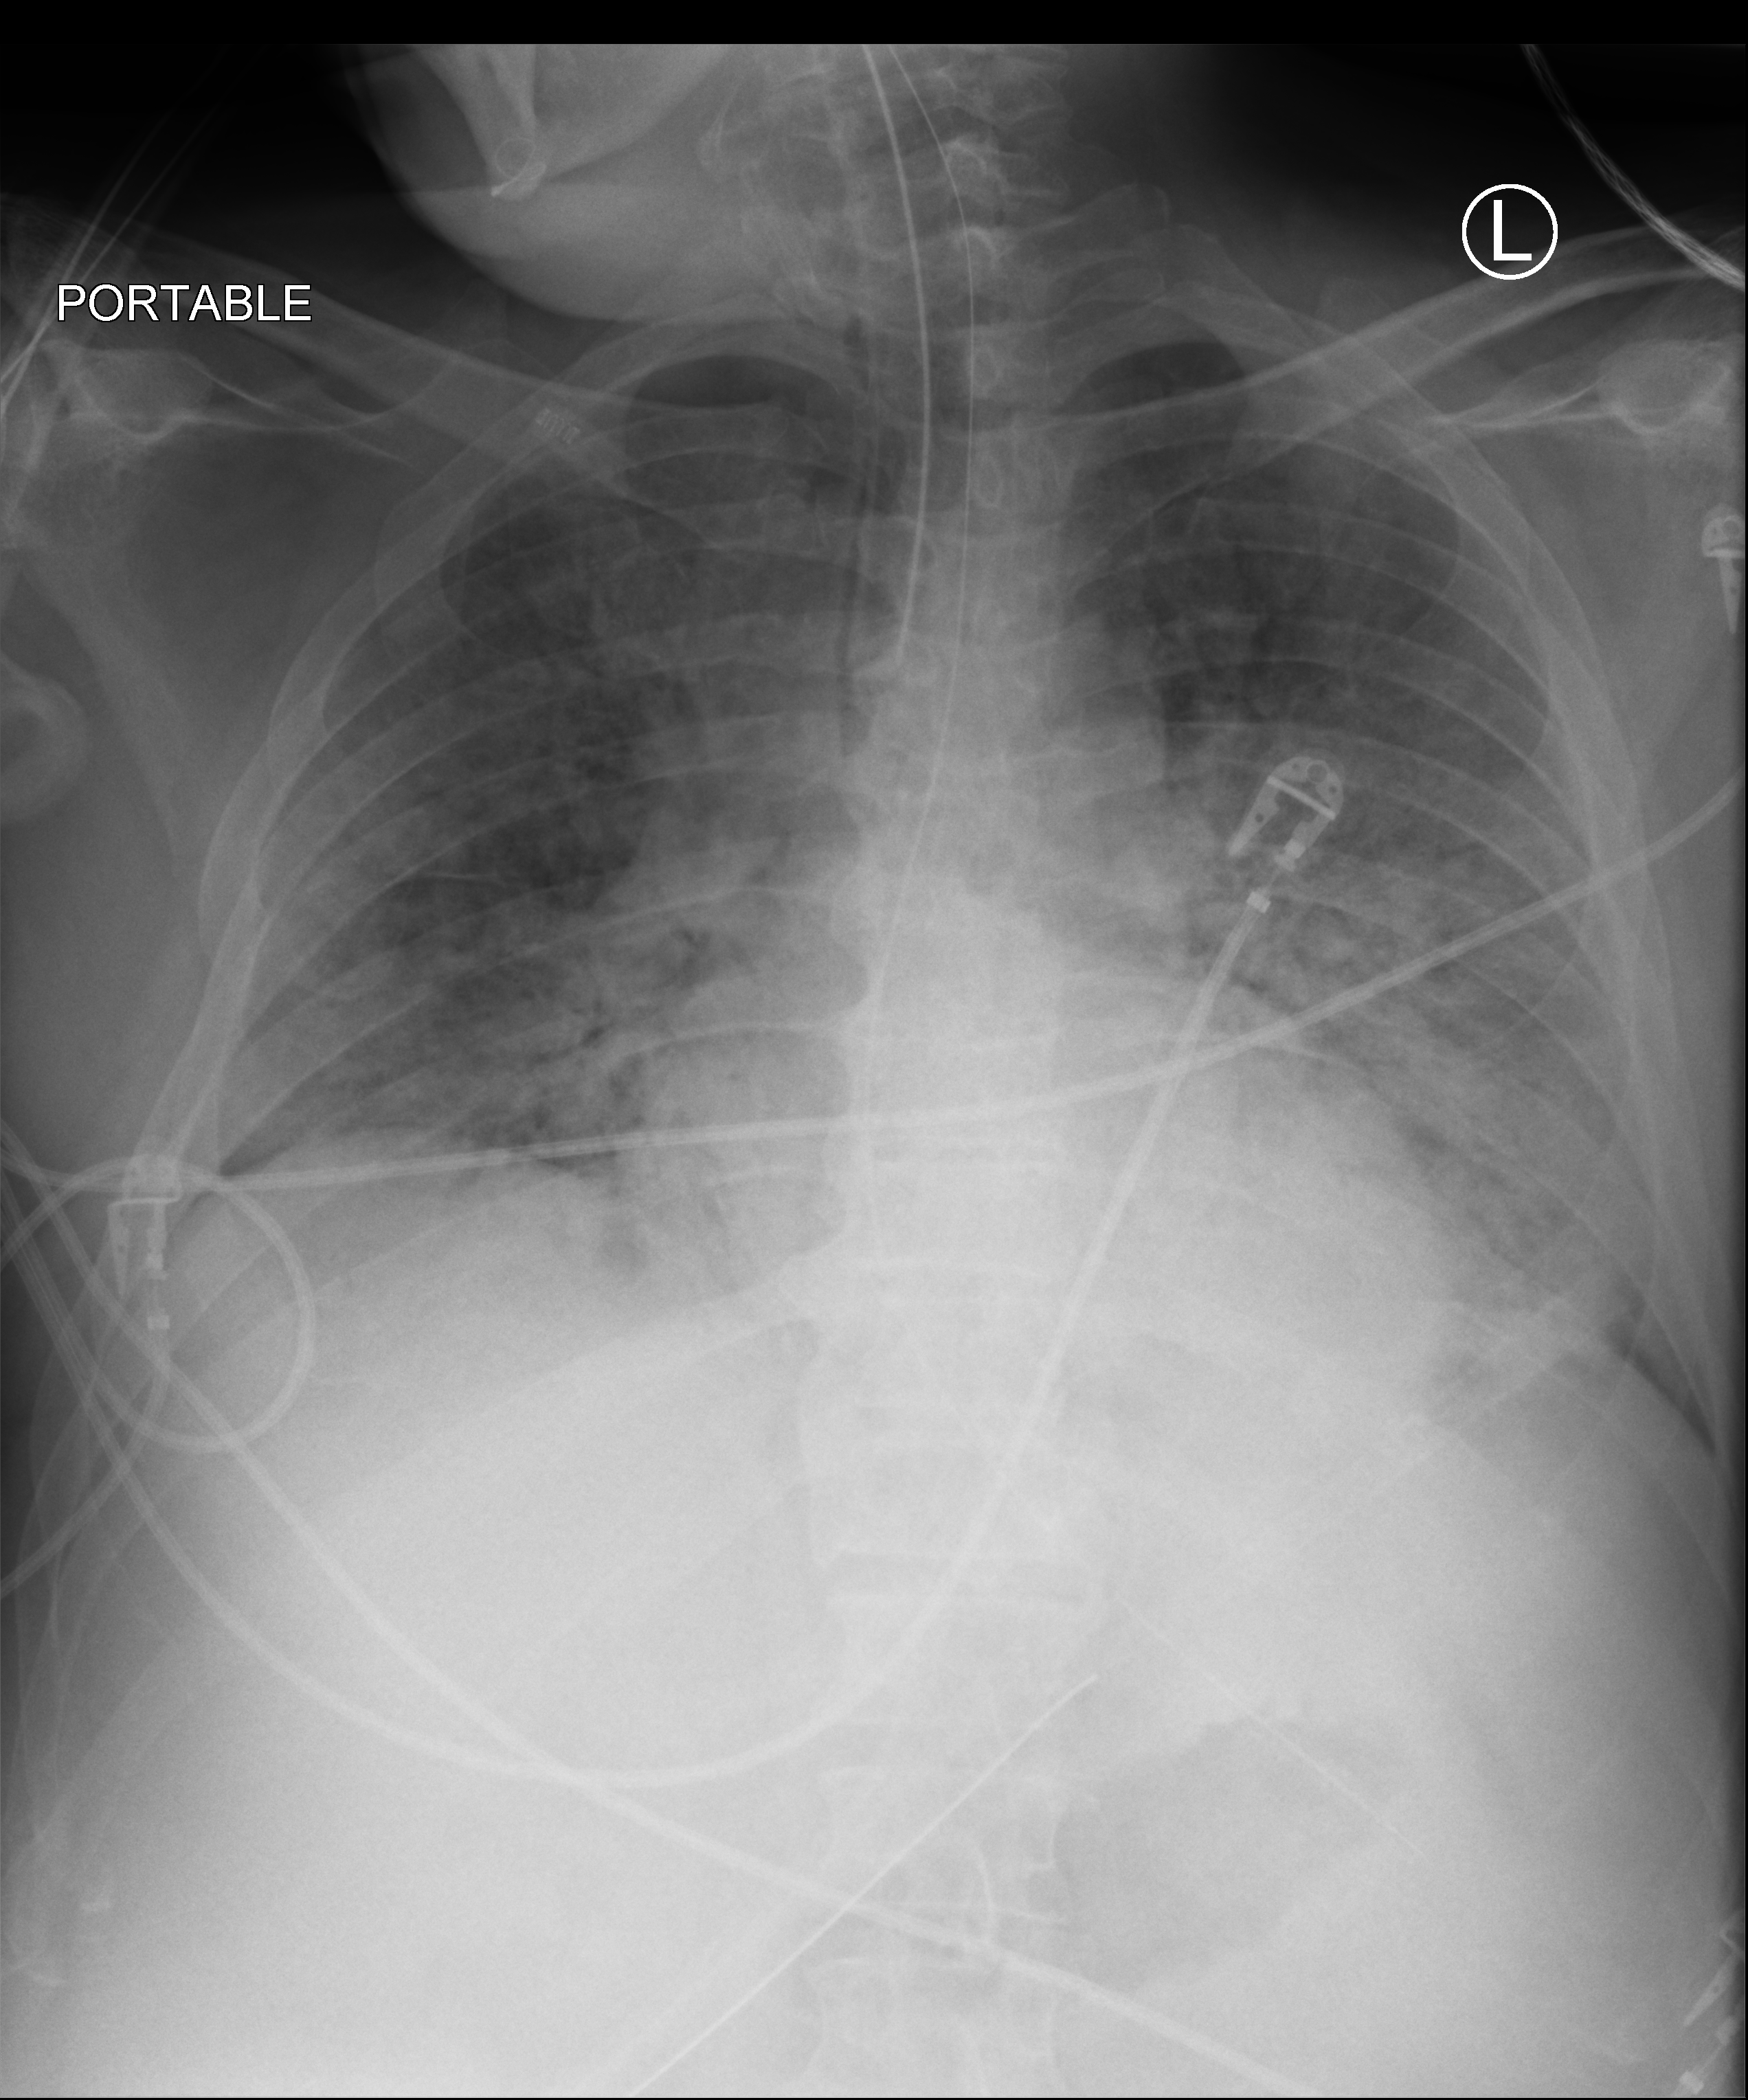
Chest X-ray (portable), anteroposterior (AP) projection. Male patient hospitalised with COVID-19, age 60–74 years.
From the hospital-stay record, not from the radiograph (when in the stay this image was taken is not recorded): COPD (admission record): no.